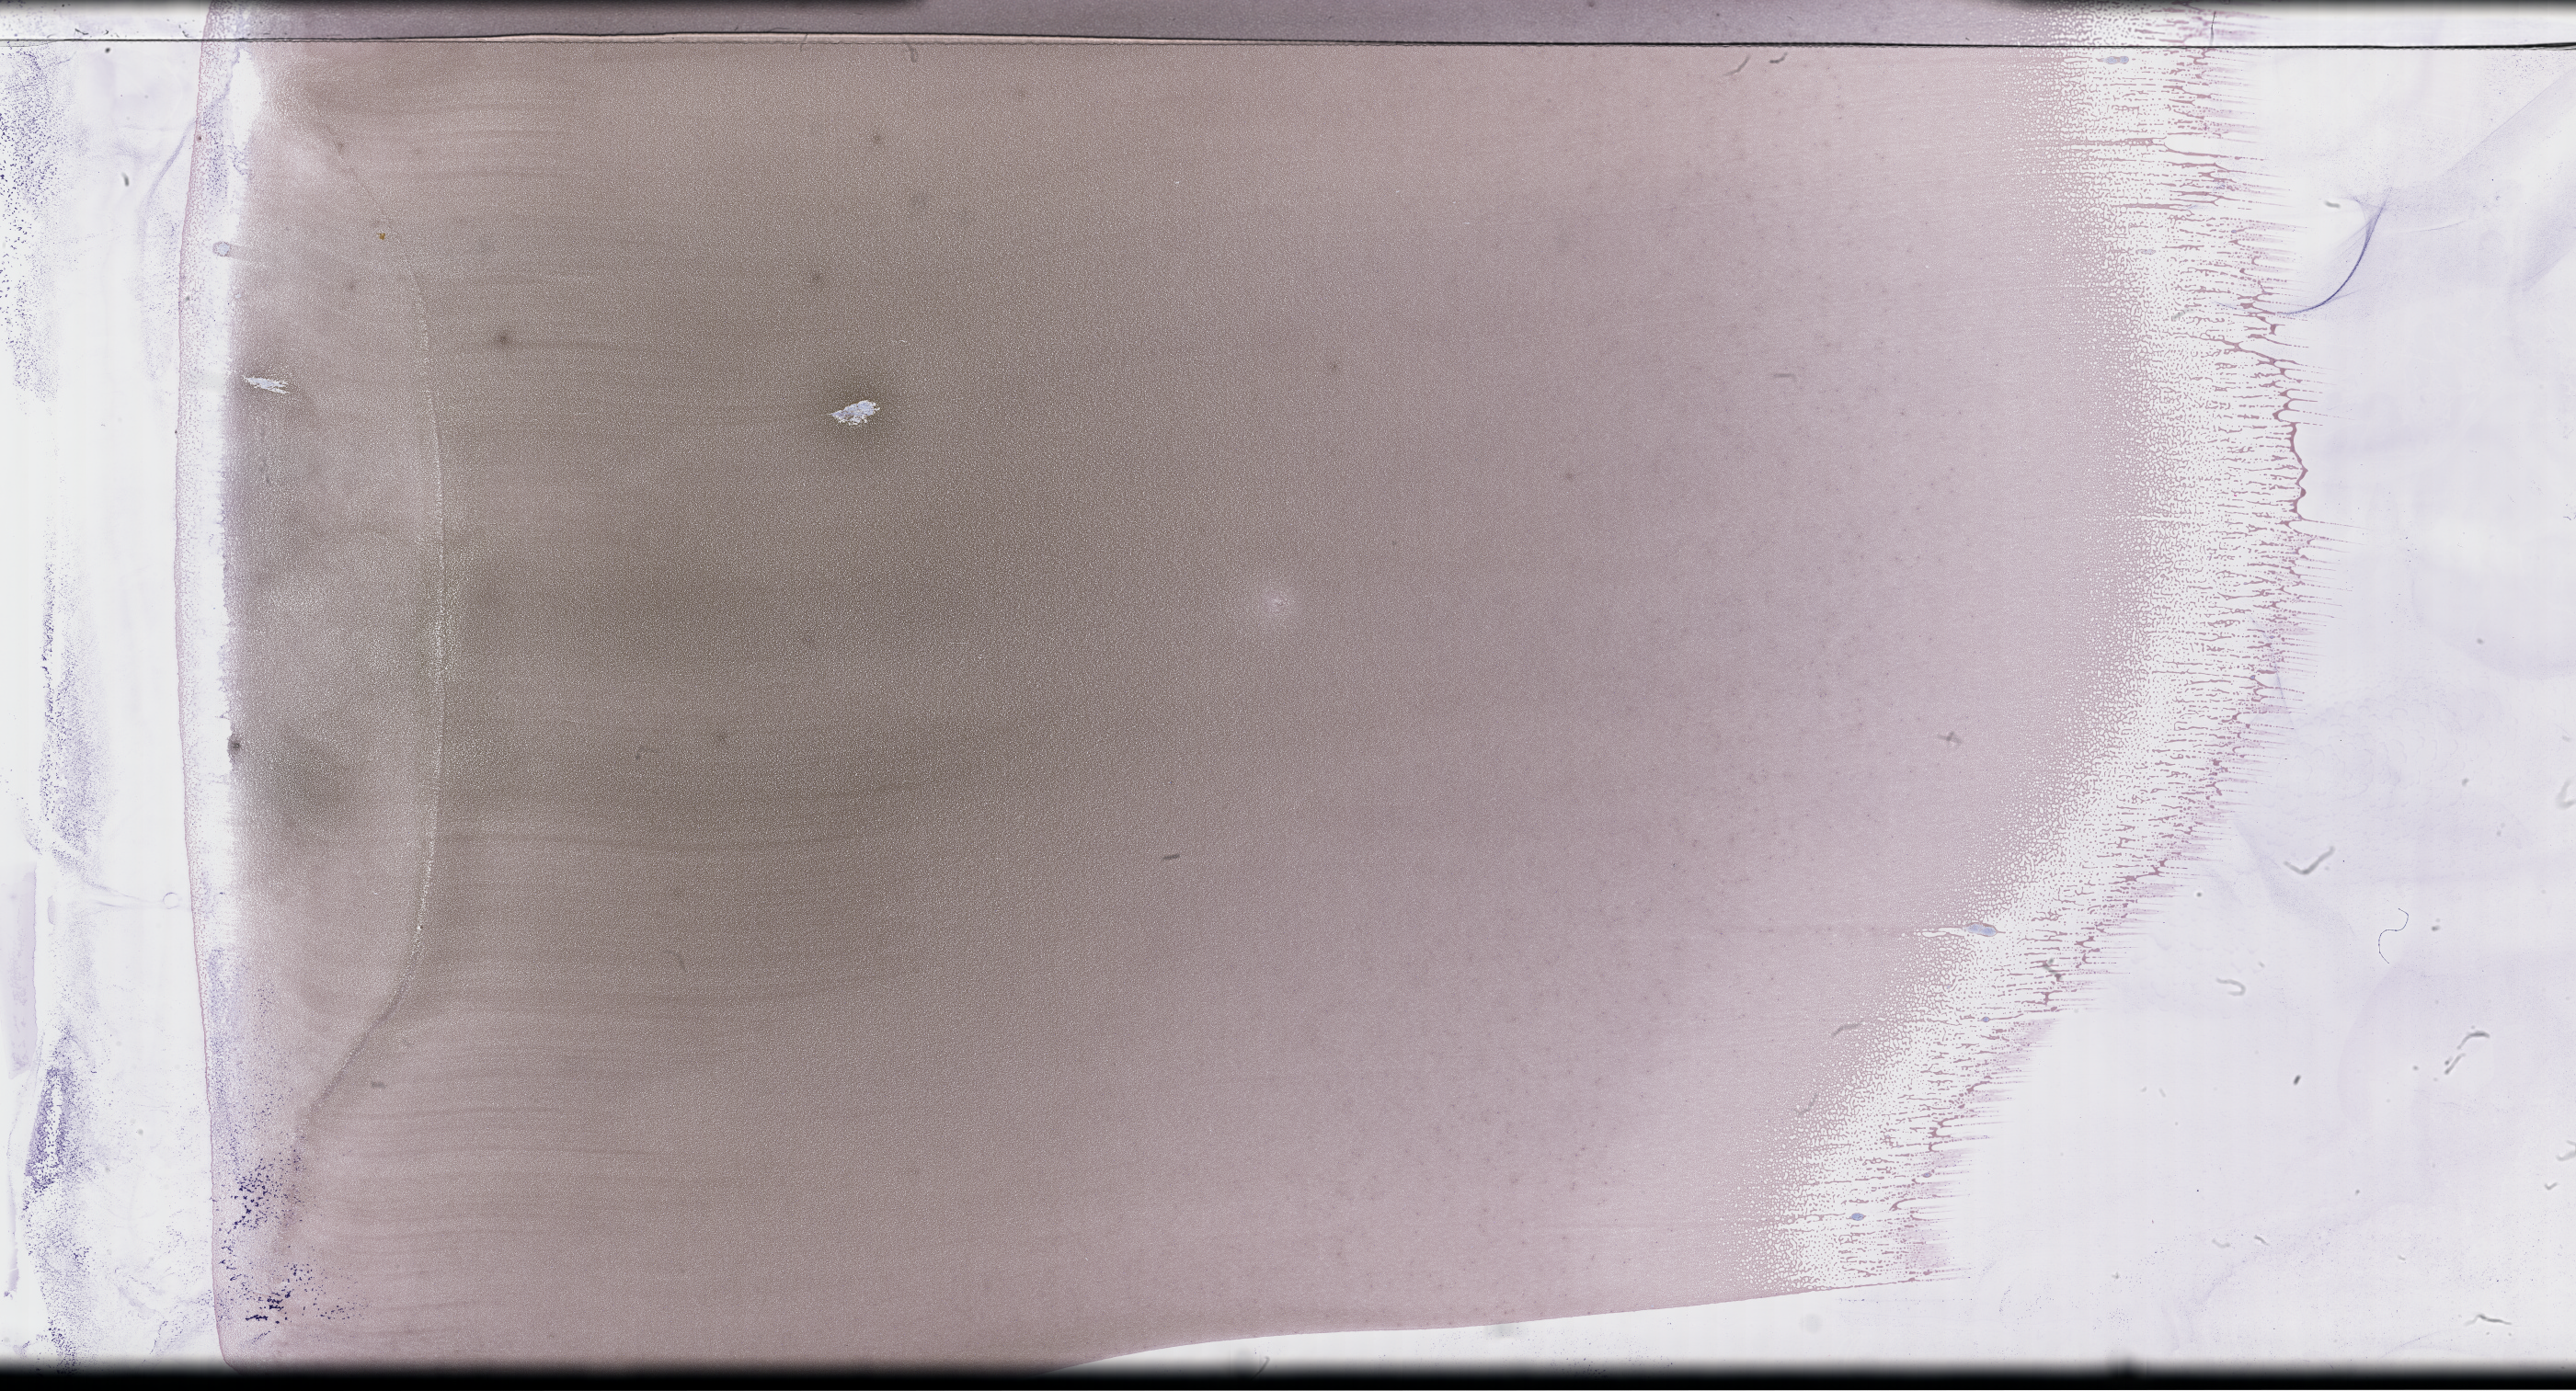
Wright–Giemsa-stained whole blood smear, whole-slide image — low-resolution overview of the scanned area, about 45.2 x 24.4 mm, smear from an EDTA sample, specimen time point: collected on treatment. Male patient.
• patient diagnosis: Plasma Cell Myeloma